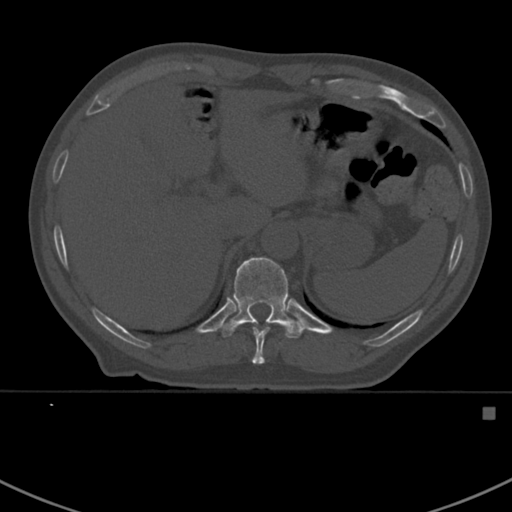
CT including the spine, one axial slice. Slice 355 of 412 in the series (ordered by position). Bone window (W 1800 / L 400 HU). 1.5 mm slice thickness. 512 × 512 image matrix, field of view 358 × 358 mm. Patient: male, 59 years. Case-level facts recorded for this patient, not image findings: primary cancer: prostate.
Structures marked on this image (semi-automatically segmented with operator editing):
- T10 vertebra: box from (x=252, y=327) to (x=270, y=364) px
- T11 vertebra: (x=219, y=257)–(x=304, y=339)